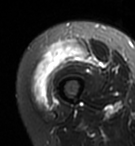
MRI of an extremity soft-tissue mass, one axial slice. Slice 18 of 95 in the series (ordered by position). T2-weighted fat-saturated. MR volume resampled by the dataset authors to the PET/CT grid (not the native acquisition matrix). 135 × 146 image matrix, field of view 132 × 143 mm. Female patient. Case-level facts recorded for this patient, not image findings: histological type: pleiomorphic undifferentiated sarcoma; grade: high; site of the primary tumour: right quadricep.
Outlined on this slice (expert contour drawn on MRI and transferred to this co-registered scan by the dataset authors):
- gross tumour volume including surrounding oedema: bounding box [x1, y1, x2, y2] px = [32, 40, 86, 105]